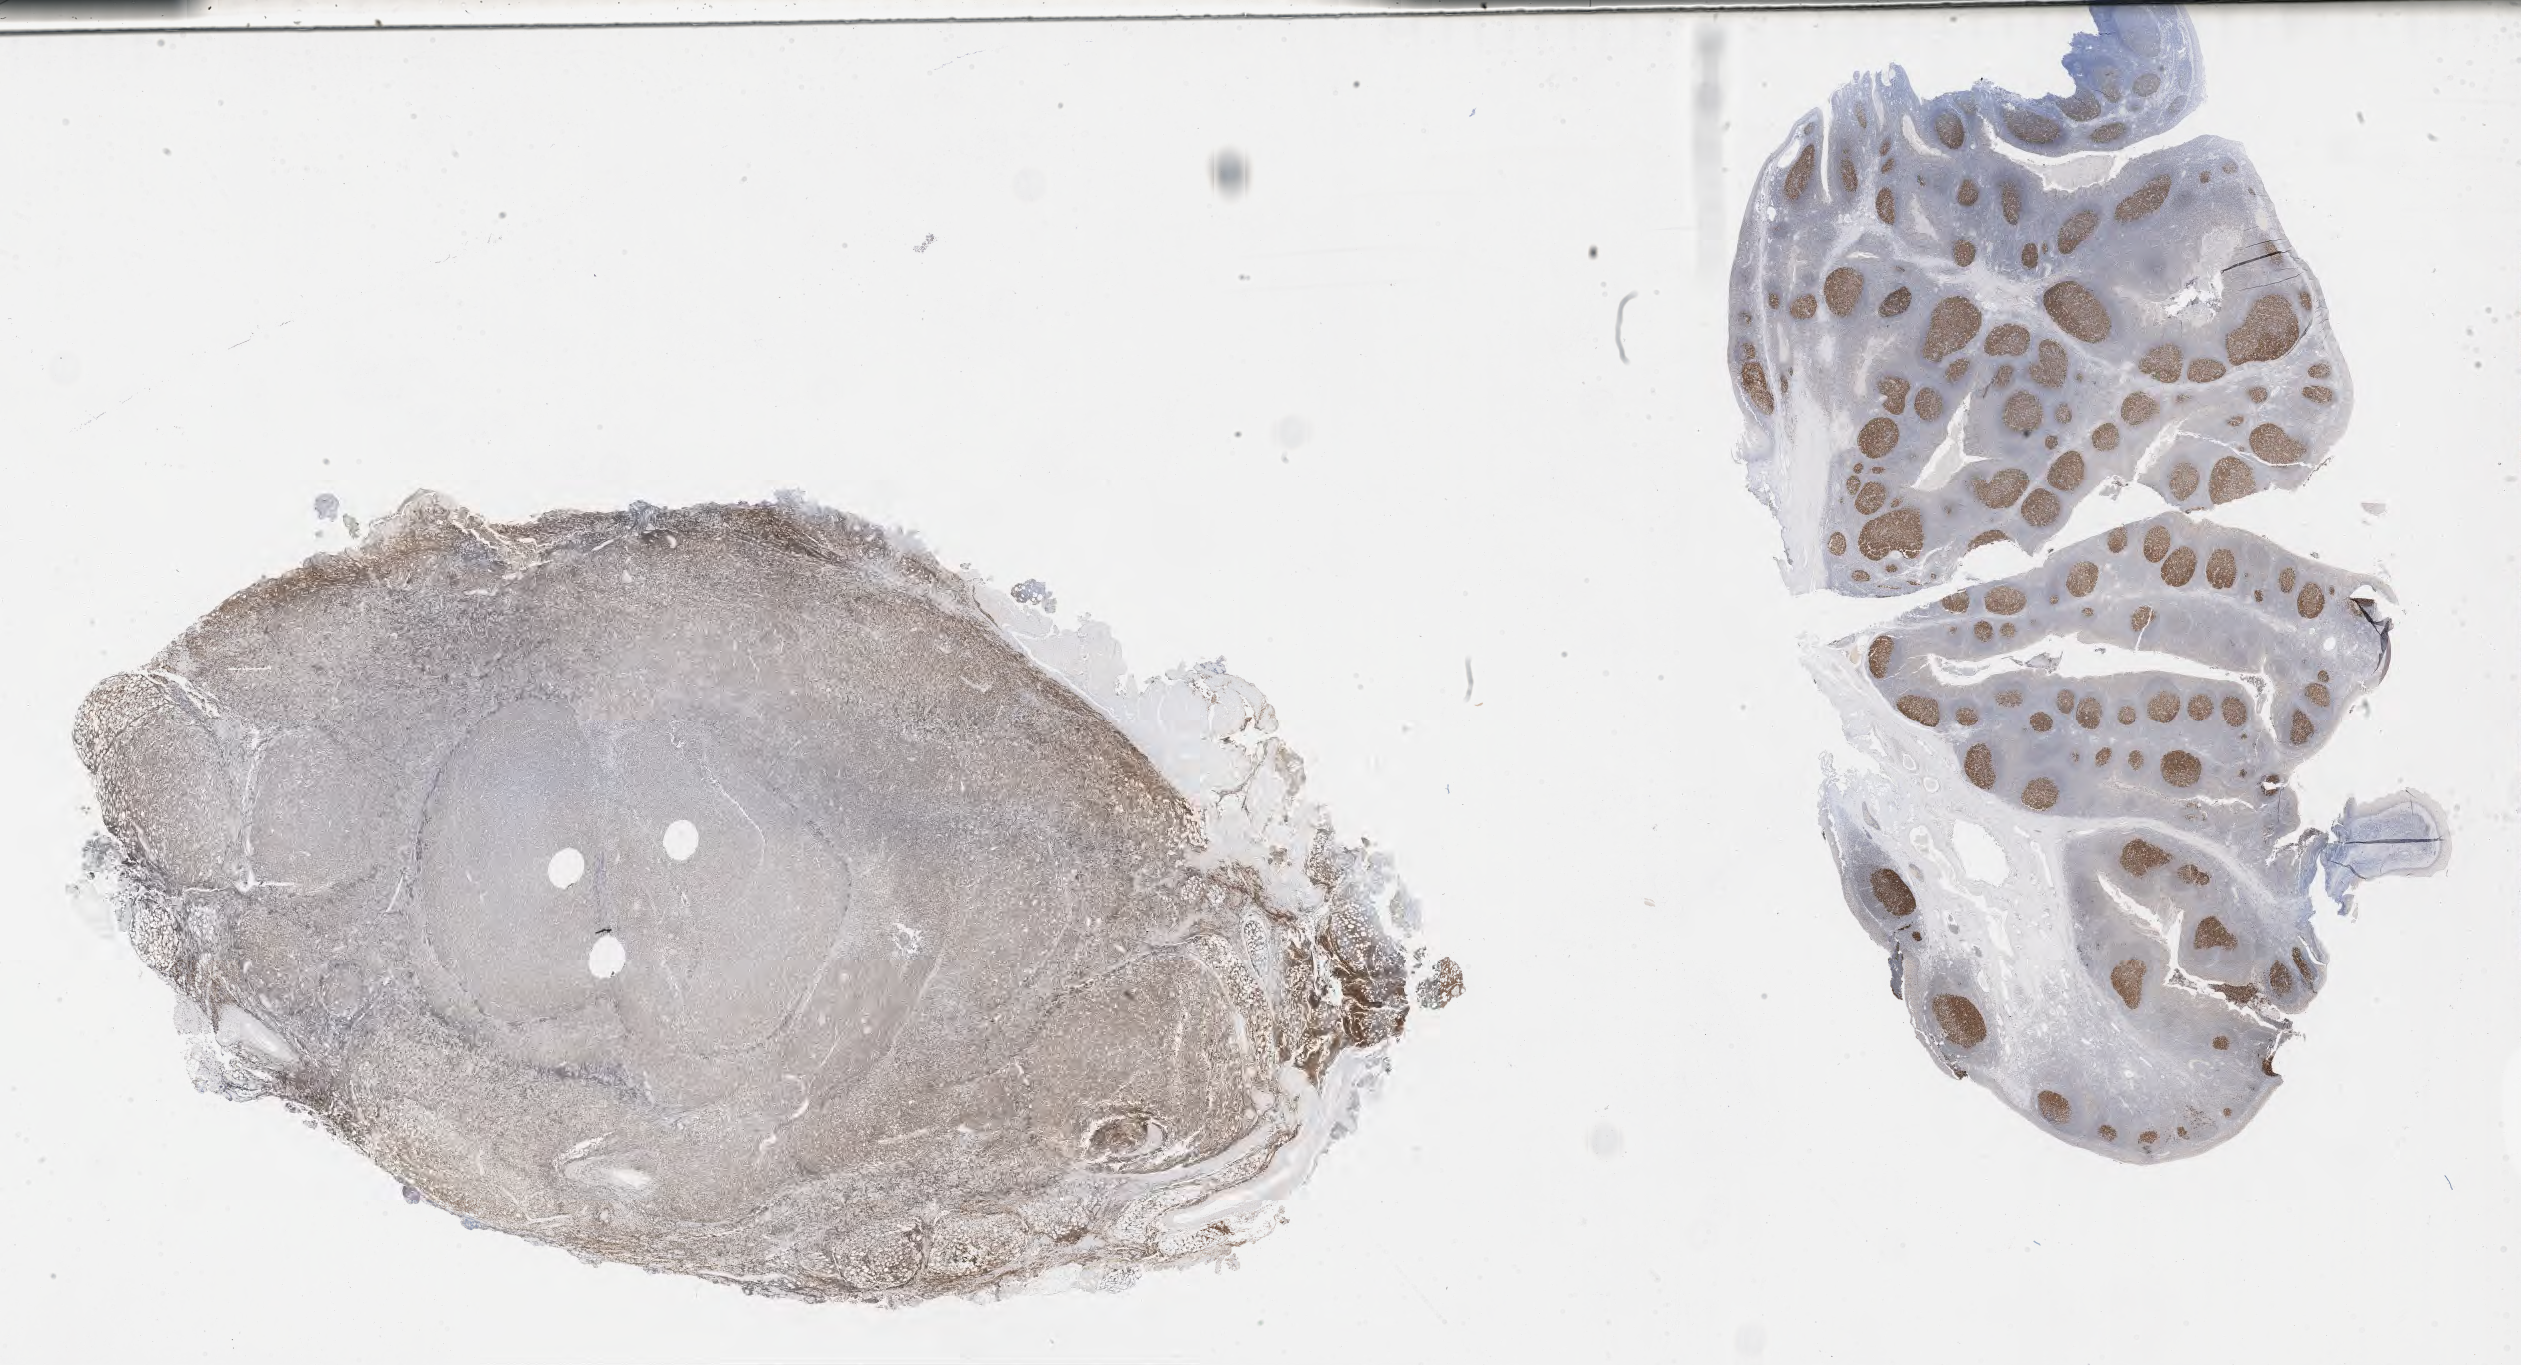
Immunohistochemistry (IHC) whole-slide image stained for BCL6, a low-resolution overview of the entire scanned area, about 40.7 x 22.1 mm, tumor tissue. Patient: male, age at initial diagnosis 4 years.
- diagnosis: Burkitt lymphoma, NOS